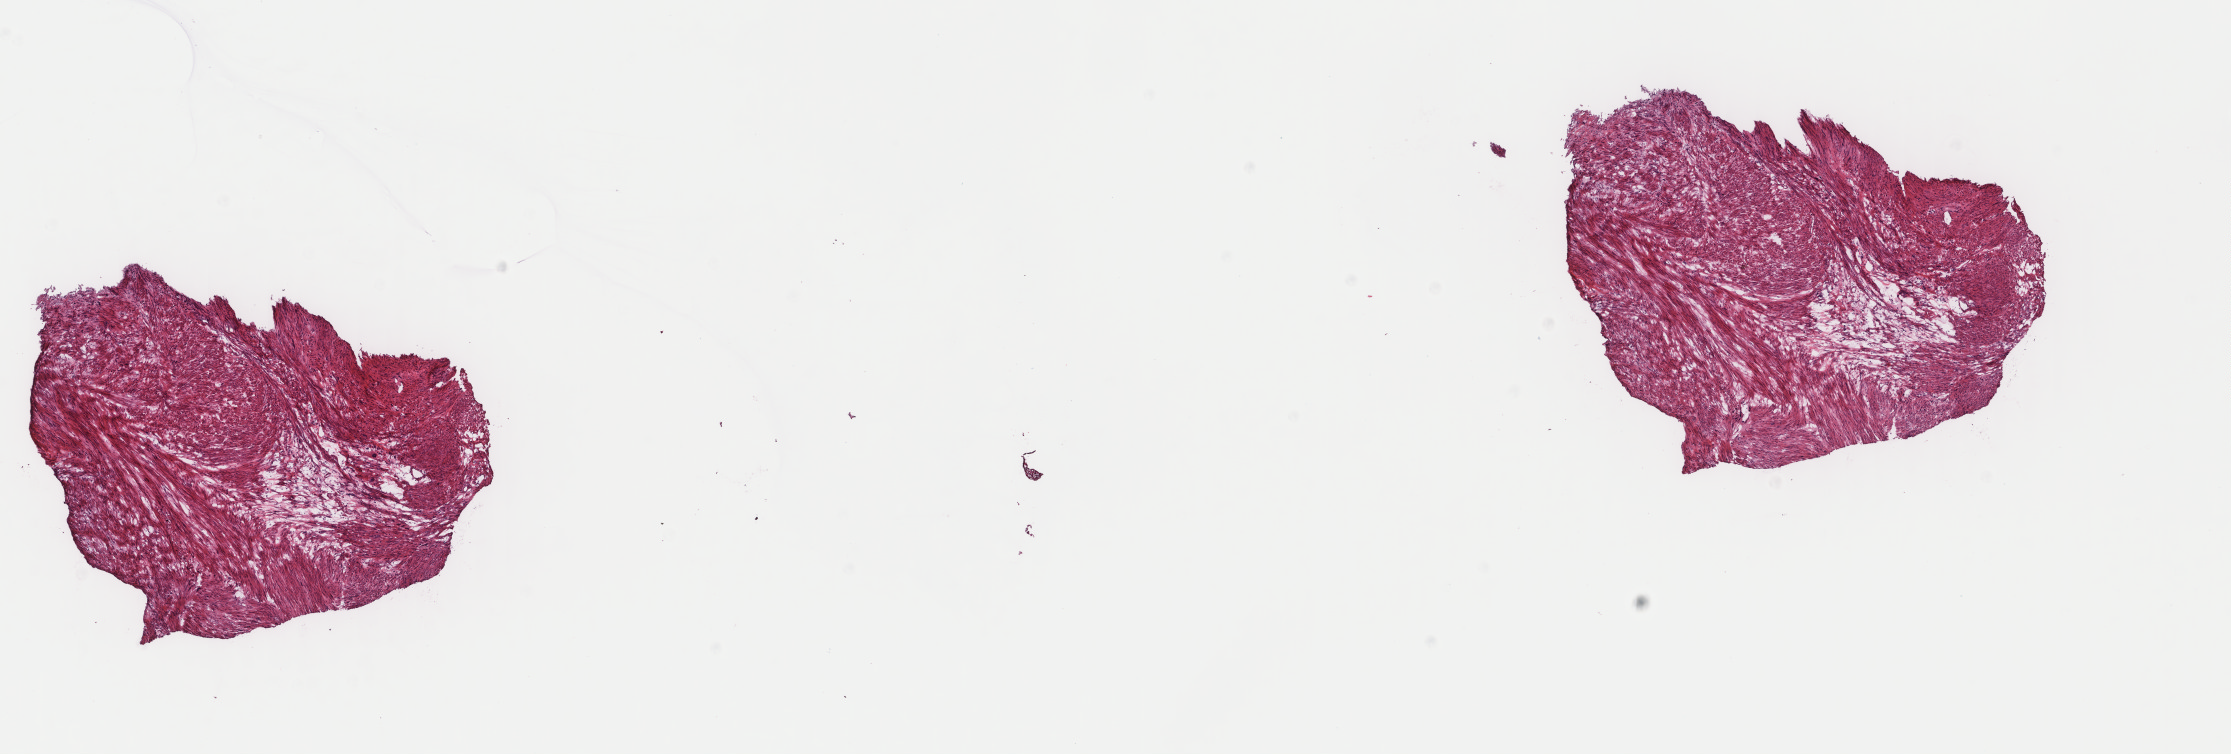
H&E-stained whole-slide image, low-resolution overview of the scanned area, about 17.7 x 6.0 mm (acquisition: 40x scan); frozen section from the top of the tissue portion; uterus, primary tumour sample. Female patient; age at initial diagnosis 64 years.
Diagnosis: Leiomyosarcoma, NOS.